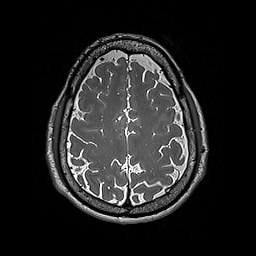
Brain MRI from a brain-tumour surgery series, one axial slice. Position 67 of 192 along the scan axis. 1 mm slice thickness. 256 × 256 image matrix. Case-level facts recorded for this patient, not image findings: histopathology: Astrocytoma; WHO grade: 2; IDH mutation: yes.
Structures marked on this image (expert manual segmentation):
- tumour: bounding box [x1, y1, x2, y2] px = [159, 114, 167, 121]